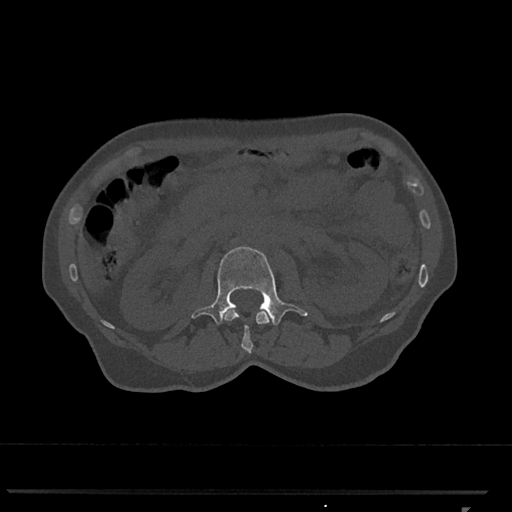
CT including the spine, one axial slice. Slice 357 of 793 in the series (ordered by position). Reconstruction kernel Br40s/3. 120 kVp. Bone window (W 1800 / L 400 HU). 0.5 mm slice thickness. 512 × 512 image matrix, field of view 380 × 380 mm. Patient: female, 62 years. Case-level facts recorded for this patient, not image findings: primary cancer: renal.
Structures marked on this image (semi-automatic segmentation, software-assisted and operator-edited):
- L1 vertebra: bounding box <224,309,272,353> (left, top, right, bottom; pixels)
- L2 vertebra: <191,246,307,325>